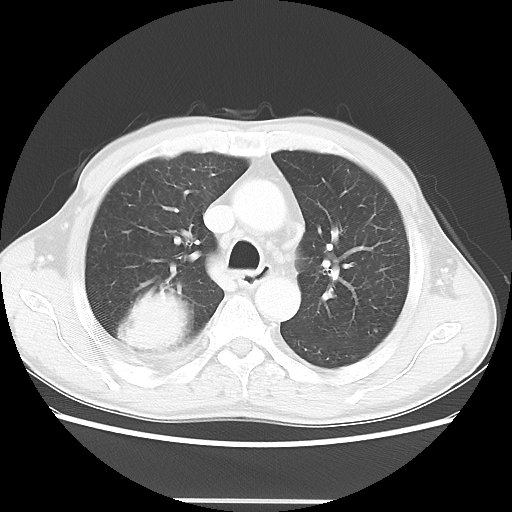
Chest CT, one axial slice. Position 35 of 48 along the scan axis. 100 kVp. Lung window (W 1500 / L -600 HU). 512 × 512 image matrix, field of view 361 × 361 mm. Patient: male, 66 years. From the clinical record (not read from this slice): clinical TNM (as recorded): T4 N1 M1; histopathological grade: G3.
Annotated regions visible in this slice (rectangle marked by the reading radiologist):
- lung tumour (recorded histology: small cell carcinoma): bounding box (x1, y1, x2, y2) in pixels: (118, 281, 201, 363)